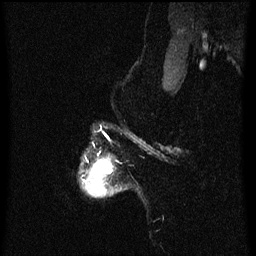
Breast MRI (dynamic contrast-enhanced), one sagittal slice; dynamic contrast-enhanced series, image 2 of 3 at this slice position (ordered by acquisition); 1.5 T; TE 4.2 ms, TR 8 ms; 256 × 256 image matrix. Female patient, age 50 years.
Structures marked on this image (semi-automatically segmented with operator editing):
- analysis volume of interest (the breast-tissue region the enhancement analysis was run in; not a lesion): bounding box <81,154,118,198> (left, top, right, bottom; pixels)
- tumour enhancement mask (voxels above the 70 % enhancement threshold inside the analysis volume of interest): <83,159,112,183>